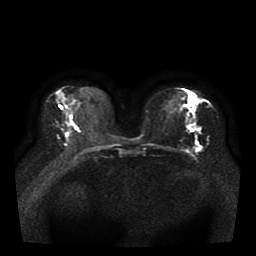
Breast MRI, one axial slice. Position 17 of 41 along the scan axis. Diffusion-weighted series; image 2 of 4 stored at this slice position (different b-values; order by instance number). 1.5 T. 5 mm slice thickness. 256 × 256 image matrix. Female patient.
Annotated regions visible in this slice (manually delineated by an expert):
- tumour on diffusion-weighted imaging: bounding box <191,107,196,111> (left, top, right, bottom; pixels)